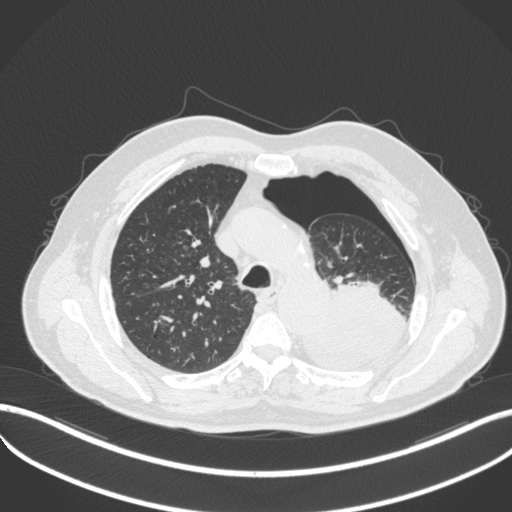
Chest CT, one axial slice. Reconstruction kernel B31f. Lung window (W 1500 / L -600 HU). 512 × 512 image matrix, field of view 400 × 400 mm. Male patient, age 76 years. Case-level facts recorded for this patient, not image findings: clinical TNM (as recorded): T3 N0 M1b.
Outlined on this slice (rectangle marked by the reading radiologist):
- lung tumour (recorded histology: adenocarcinoma): box from (x=295, y=273) to (x=419, y=368) px